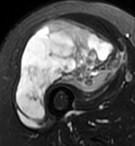
MRI of an extremity soft-tissue mass, one axial slice. Slice 55 of 95 in the series (ordered by position). T2-weighted fat-saturated. MR volume resampled by the dataset authors to the PET/CT grid (not the native acquisition matrix). 3.27 mm slice thickness. 135 × 146 image matrix, field of view 132 × 143 mm. Female patient. From the clinical record (not read from this slice): histological type: pleiomorphic undifferentiated sarcoma; grade: high; site of the primary tumour: right quadricep.
Structures marked on this image (expert contour drawn on MRI and transferred to this co-registered scan by the dataset authors):
- gross tumour volume including surrounding oedema: bounding box (x1, y1, x2, y2) in pixels: (16, 18, 122, 121)
- gross tumour volume (mass): (16, 18, 122, 121)